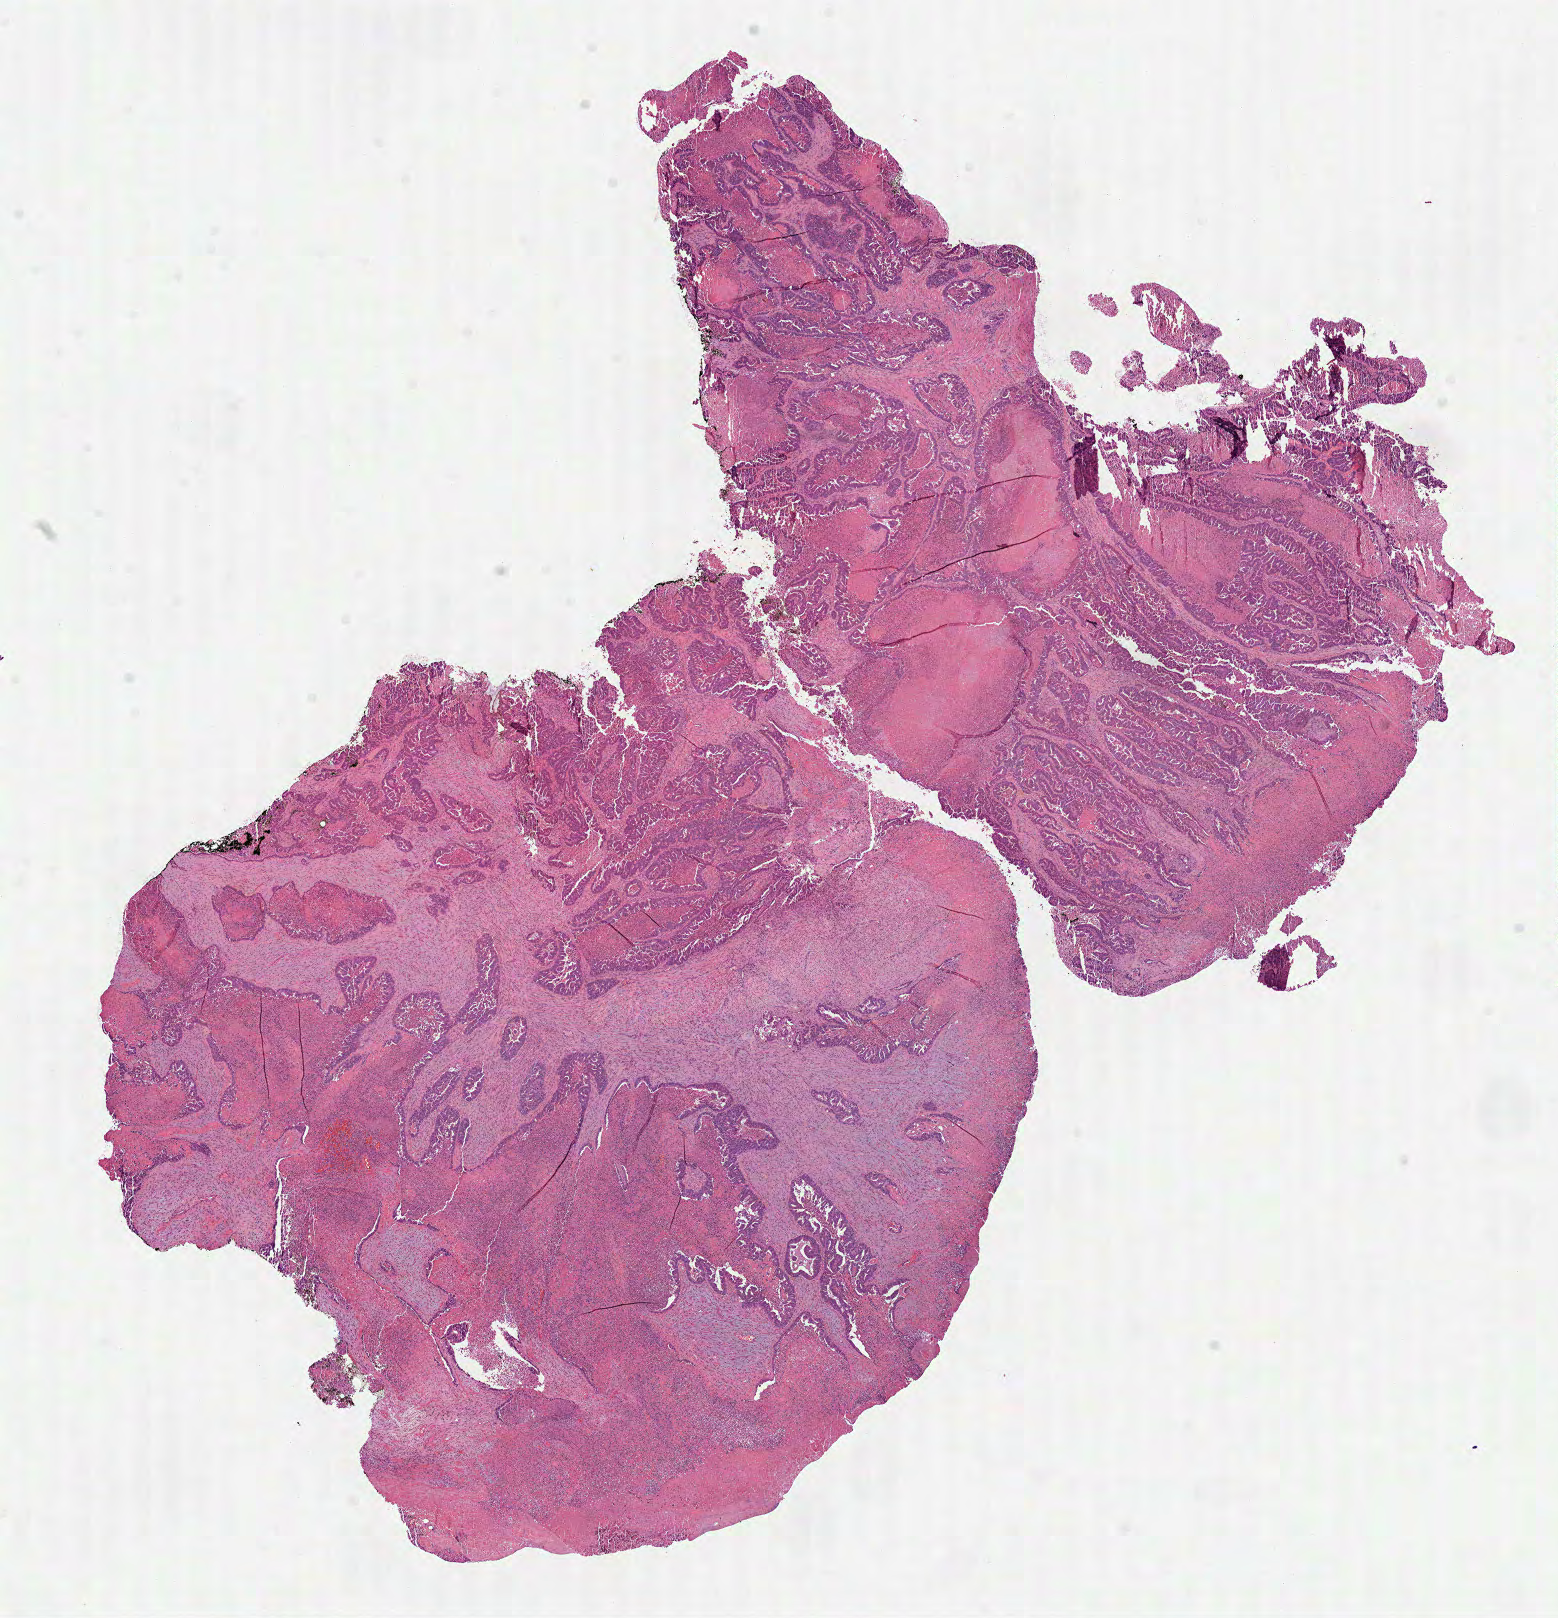
Digitized H&E-stained tissue section (whole slide), shown as a low-resolution overview of the whole scanned area (about 12.6 x 13.1 mm, slide scanned at 40x); FFPE section; primary tumour sample from the rectum. Male, age 50 years at initial diagnosis.
Diagnosis: Adenocarcinoma, NOS (rectosigmoid junction).